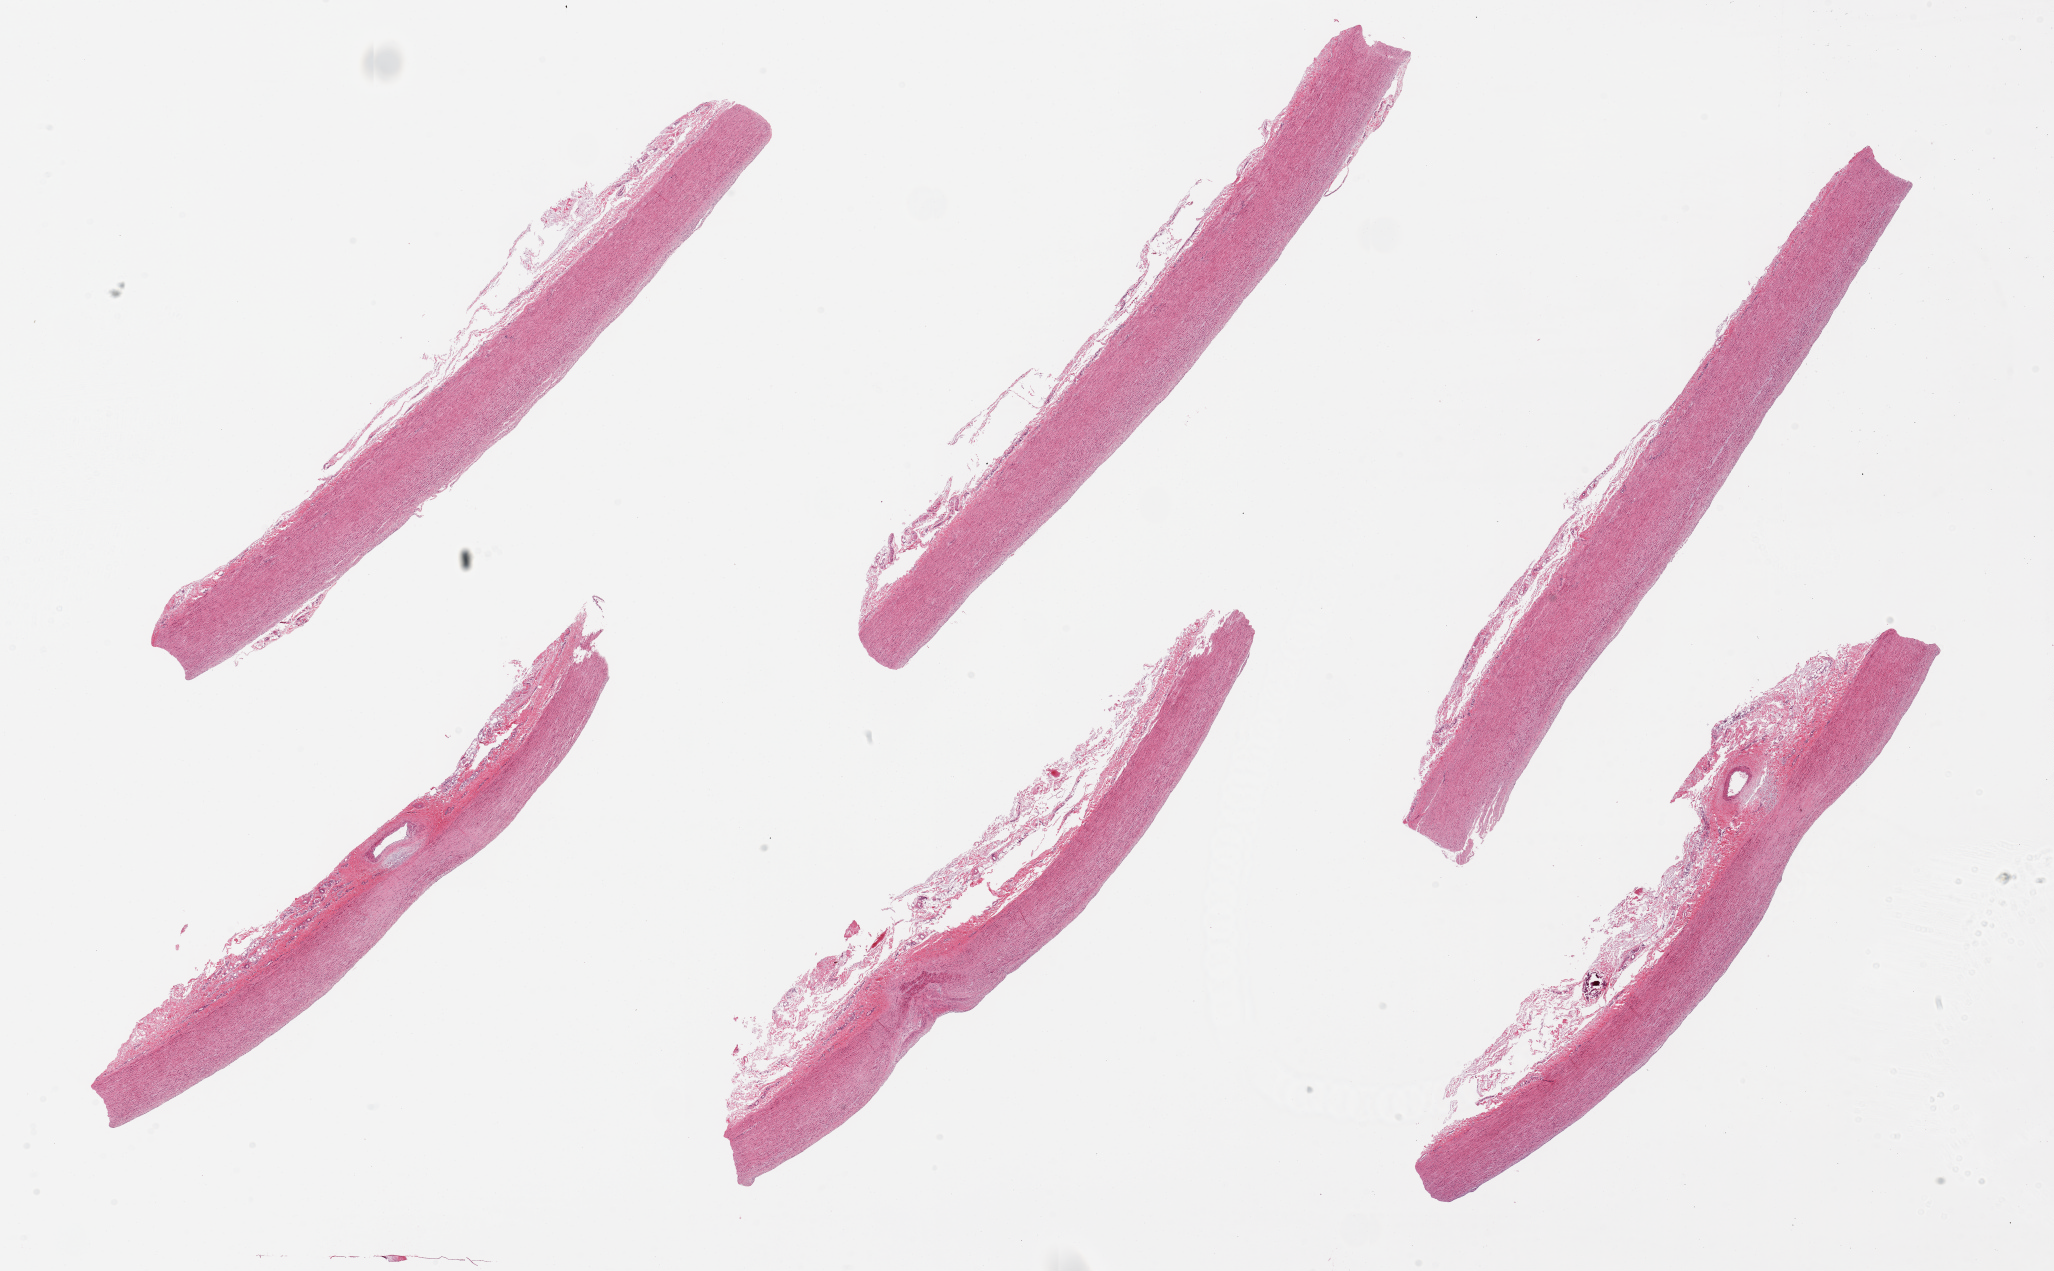
Digitized hematoxylin and eosin (H&E)-stained section — whole scanned area (about 32.5 x 20.1 mm, acquisition: 20x scan) shown as a low-resolution overview; PAXgene-fixed paraffin-embedded (PFPE) section; target tissue: aorta; tissue donor sample. Donor sex: female.
- review note (as recorded): 6 pieces, up to 13x2mm